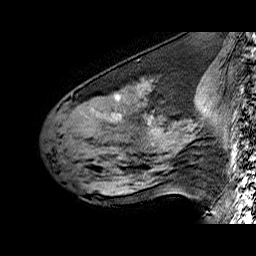
Breast MRI (dynamic contrast-enhanced), one sagittal slice. Slice 24 of 60 in the series (ordered by position). Dynamic contrast-enhanced series, time point 2 of 6 at this slice position (early post-contrast). 1.5 T. TE 6.4 ms, TR 32.9 ms. 256 × 256 image matrix. Female patient. Case-level facts recorded for this patient, not image findings: setting: breast cancer imaged before/during neoadjuvant chemotherapy; receptor status: HER2-positive.
Annotated regions visible in this slice (semi-automatic segmentation, software-assisted and operator-edited):
- analysis volume of interest (the breast-tissue region the enhancement analysis was run in; not a lesion): bounding box <51,78,196,160> (left, top, right, bottom; pixels)
- tumour enhancement mask (voxels above the 100 % enhancement threshold inside the analysis volume of interest): <111,95,152,122>